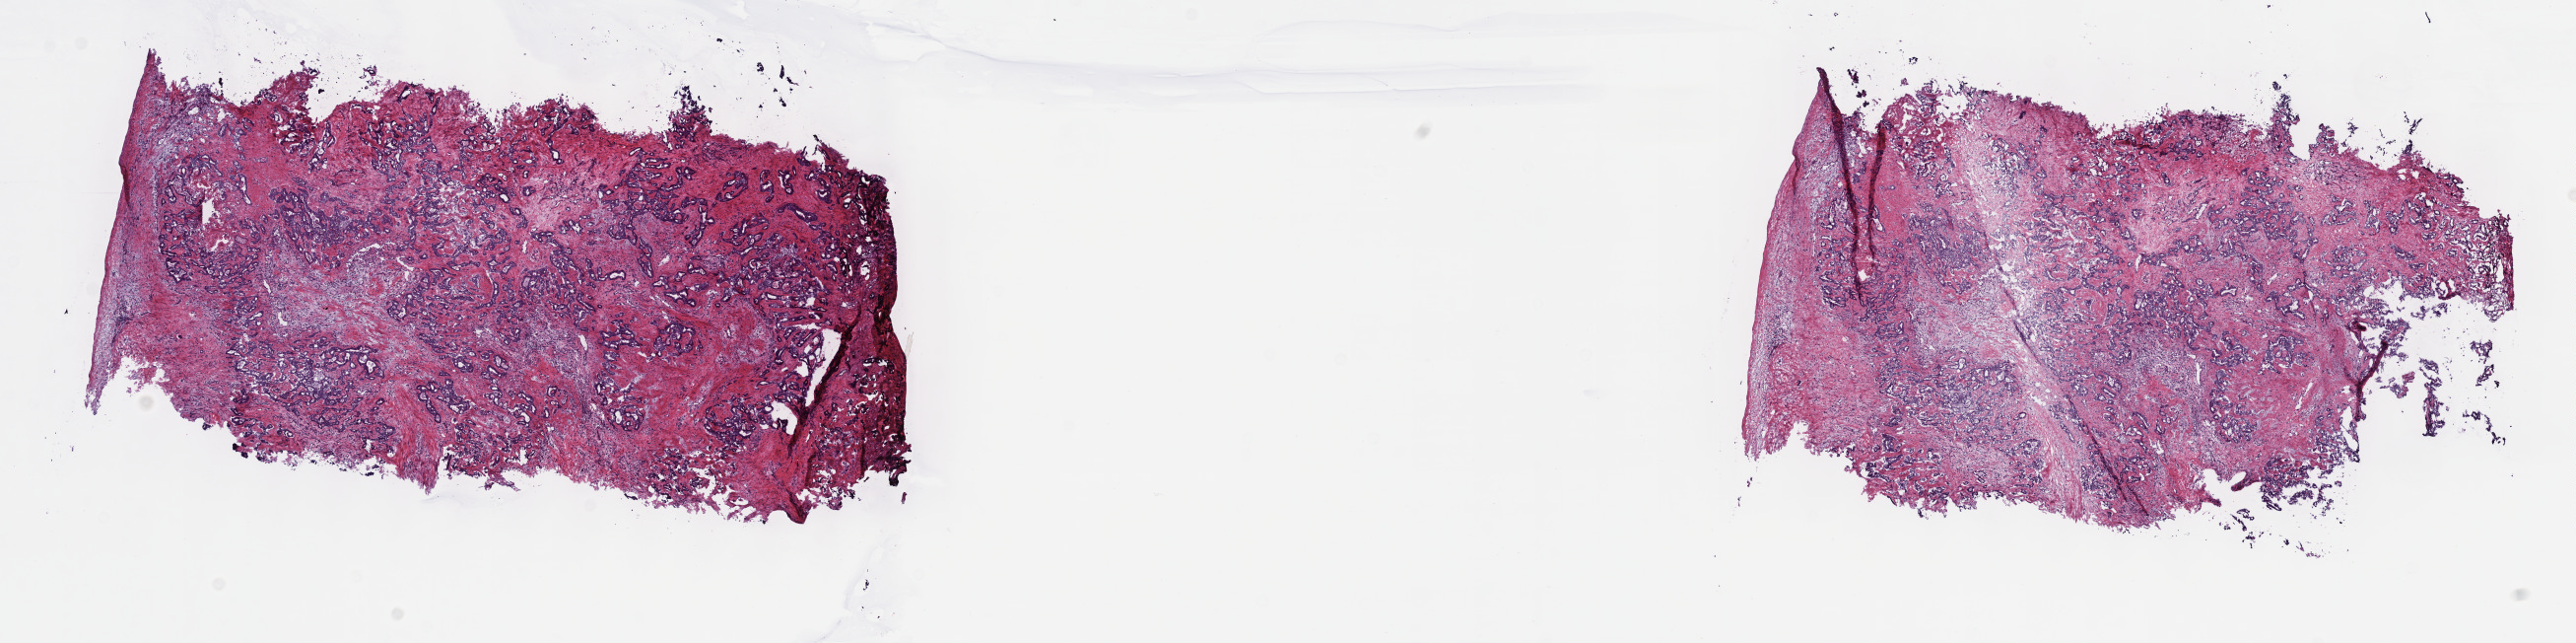
Whole-slide histology image, Hematoxylin and eosin (H&E) stained, low-resolution overview of the scanned area, about 21.1 x 5.3 mm. Frozen section. Bile duct, primary tumour sample. Patient: female, age at initial diagnosis 74 years.
Diagnosis: Cholangiocarcinoma (intrahepatic bile duct).